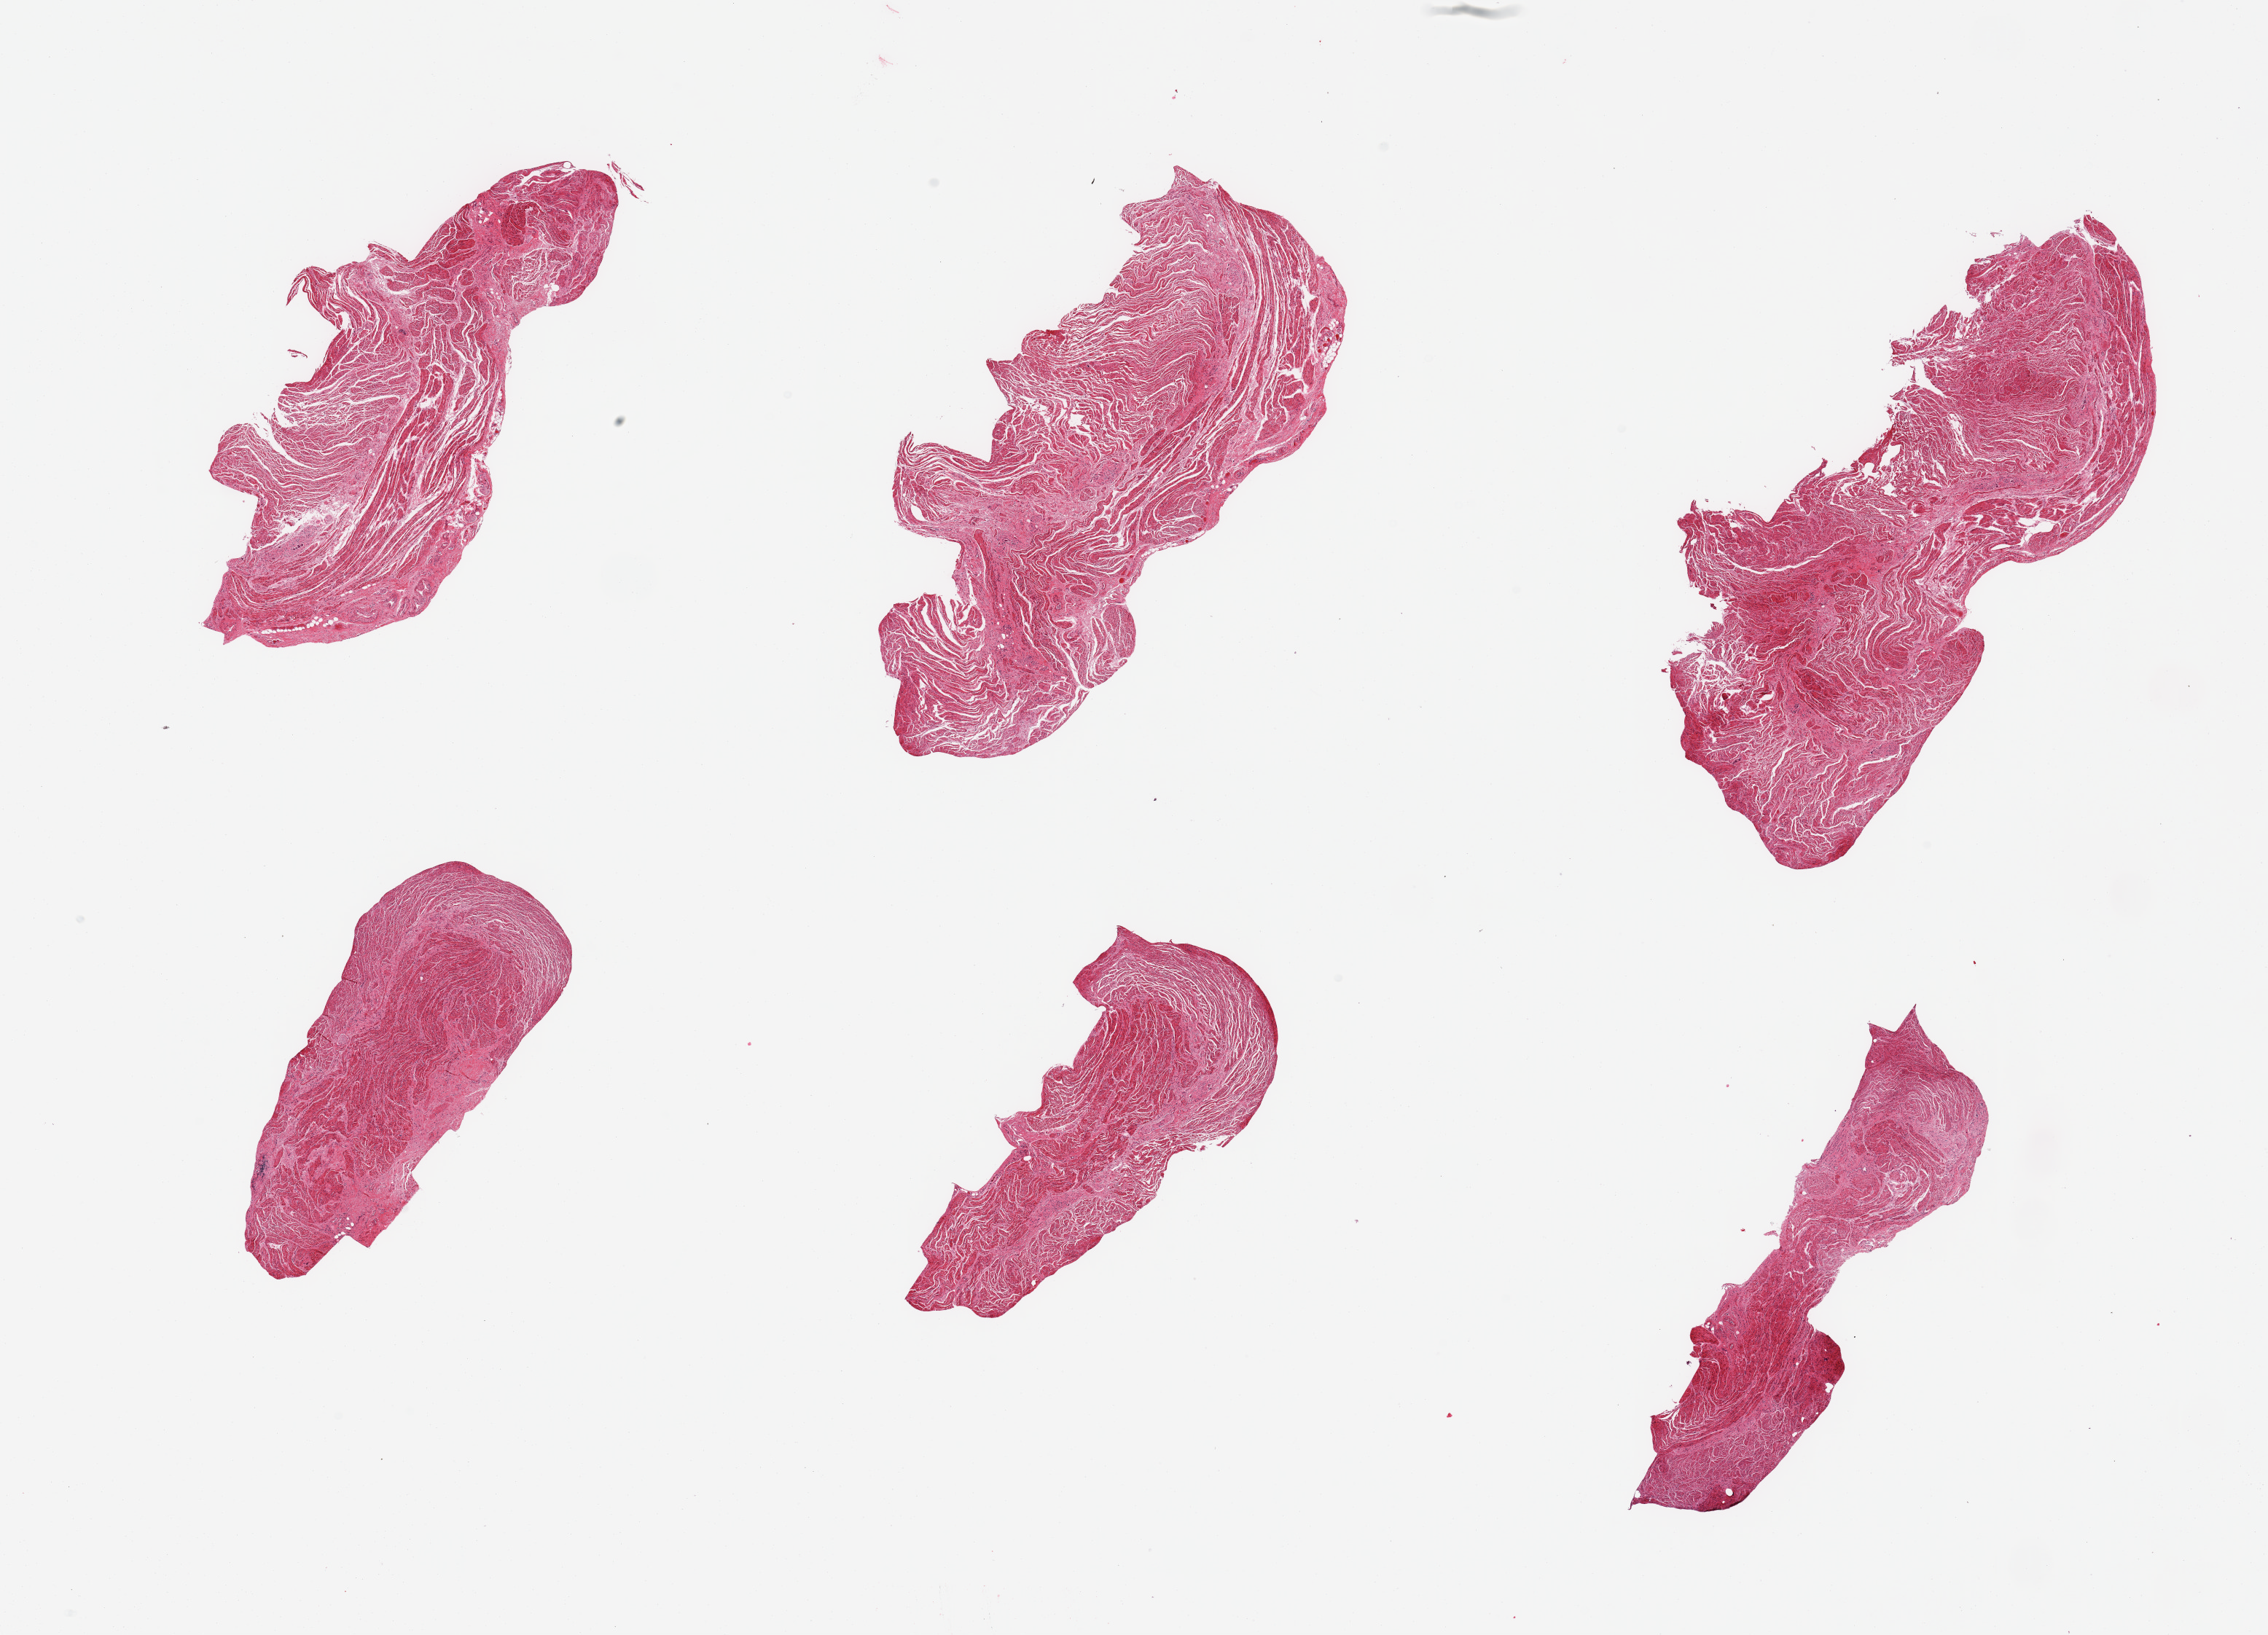
Whole-slide image, H&E stain, brightfield, whole scanned area (about 24.6 x 17.7 mm, from a 20x scan) shown as a low-resolution overview, PAXgene-fixed paraffin-embedded (PFPE) section, target tissue: gastroesophageal junction, tissue donor sample.
Reviewer comment on this tissue sample: 6 pieces; well trimmed.